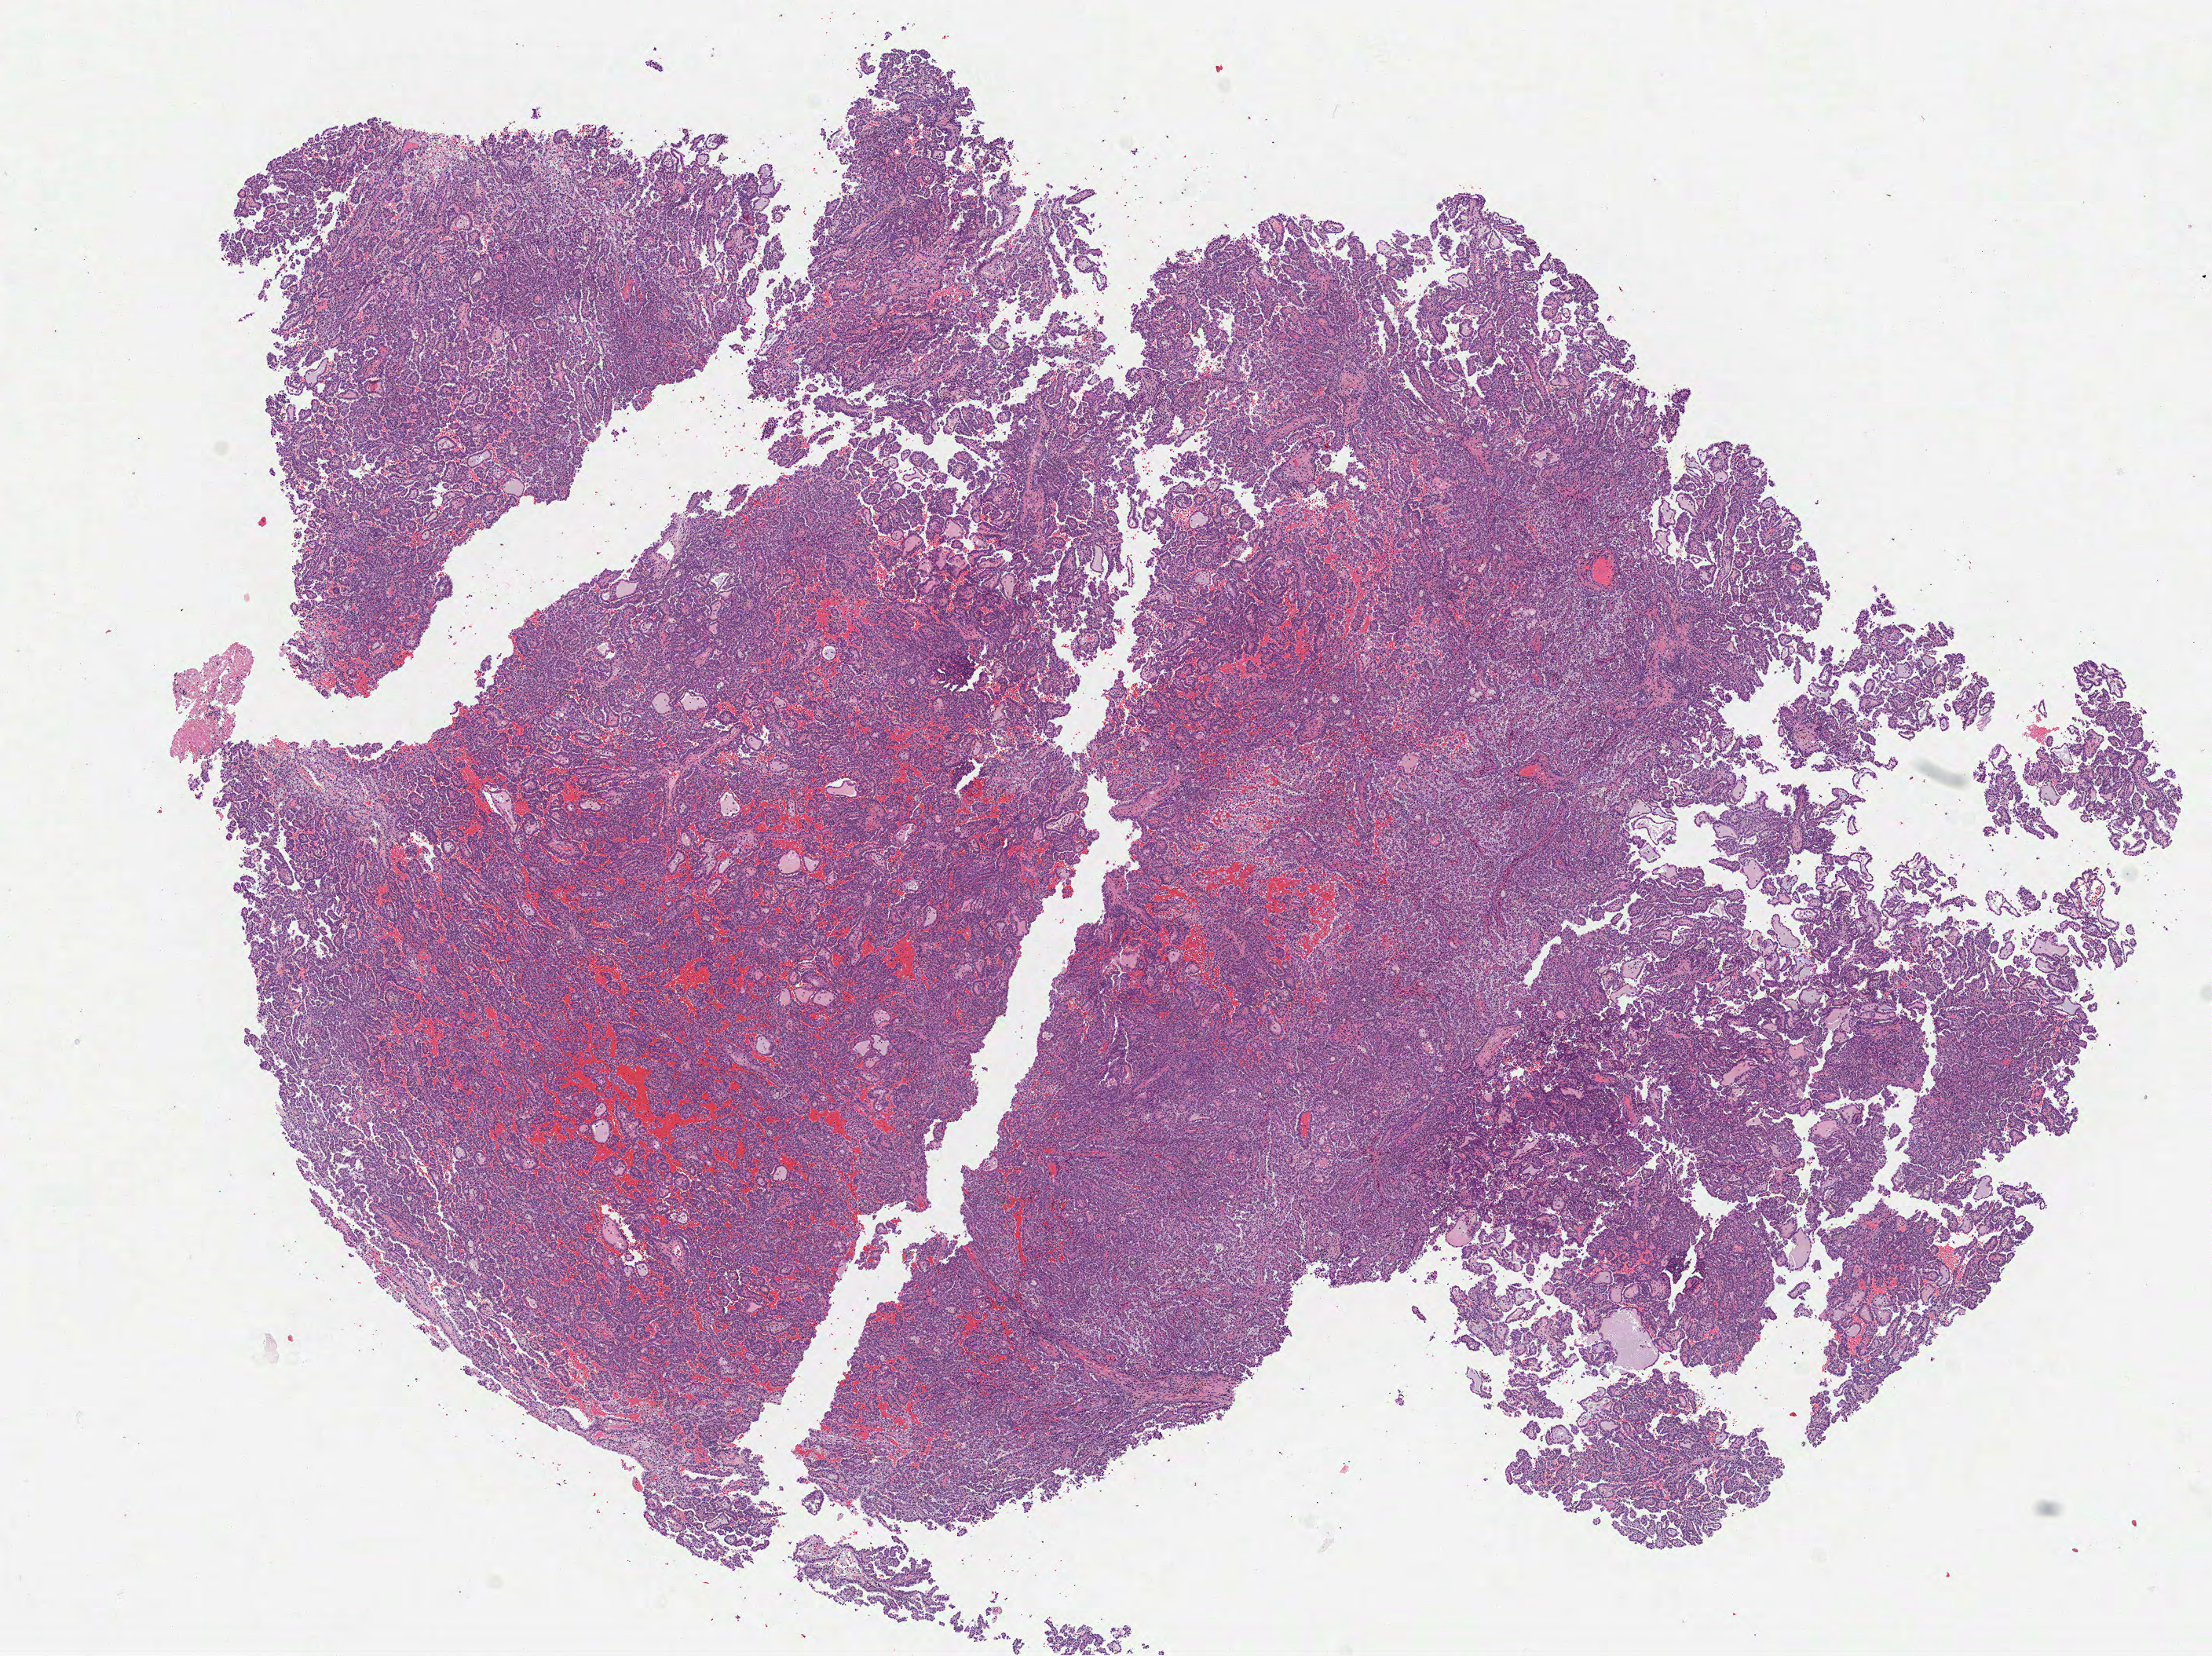
Whole-slide histology image, Hematoxylin and eosin (H&E) stained, shown as a low-resolution overview of the whole scanned area (about 11.4 x 8.5 mm, from a 40x scan). Frozen section from the top of the tissue portion. Primary tumour sample from the kidney. Male, age 63 years at initial diagnosis.
Histologic diagnosis: Papillary adenocarcinoma, NOS.